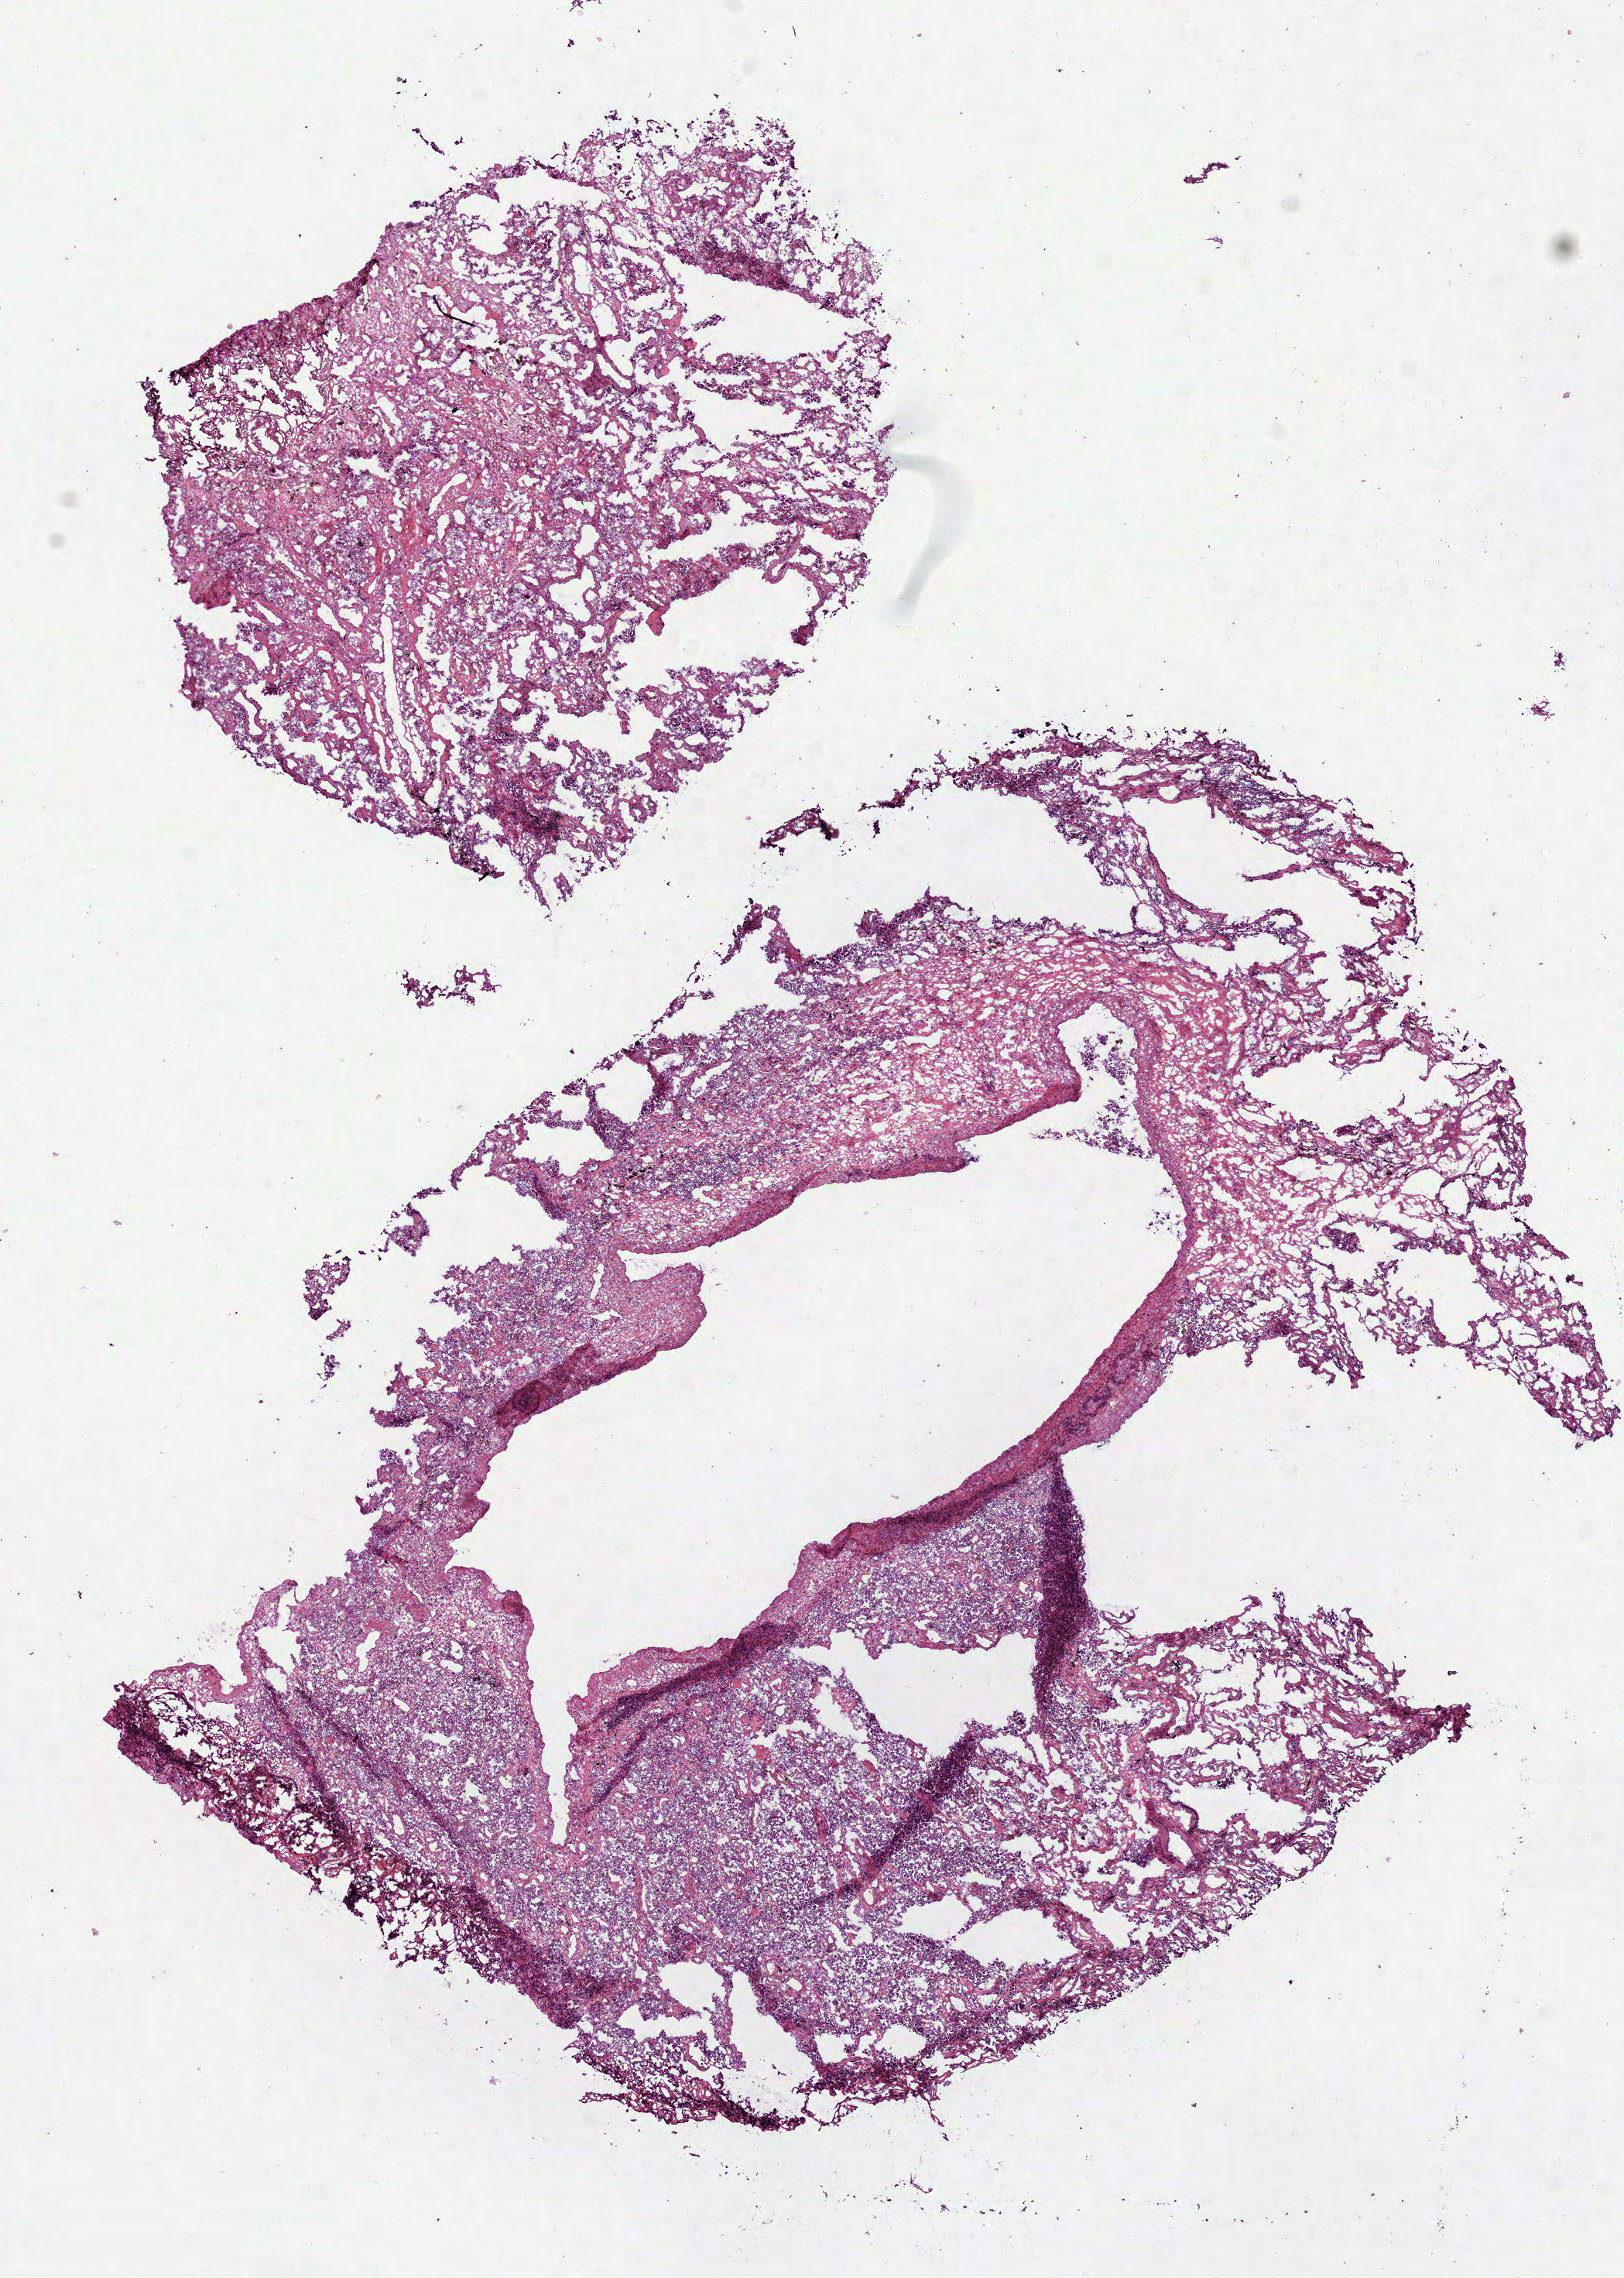
H&E-stained whole-slide image — shown as a low-resolution overview of the whole scanned area (about 8.5 x 11.9 mm). Frozen section. Lung, primary tumour sample. Female patient; age at initial diagnosis 54 years. Pathologist review of this section (percent, as recorded): tumour cells 65%, tumour nuclei 75%, normal cells 25%, stromal cells 10%, necrosis 0%.
* AJCC pathologic stage: IIB
* laterality: right
* histologic diagnosis: Adenocarcinoma, NOS